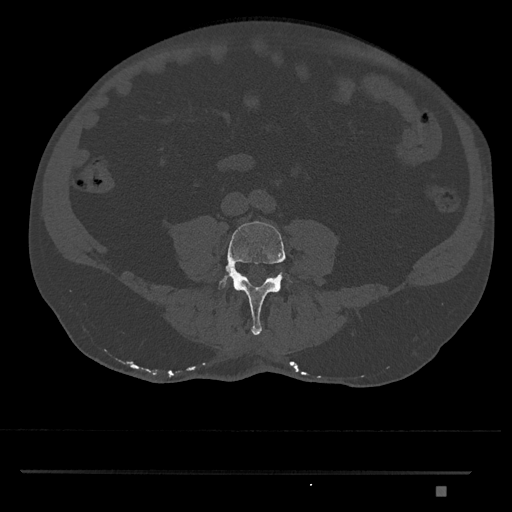
CT including the spine, one axial slice; slice 612 of 1134 in the series (ordered by position); bone window (W 1800 / L 400 HU); 0.5 mm slice thickness; 512 × 512 image matrix, field of view 429 × 429 mm. Patient: male, 65 years. From the clinical record (not read from this slice): primary cancer: prostate.
Outlined on this slice (semi-automatically segmented with operator editing):
- L4 vertebra: bounding box <218,221,292,335> (left, top, right, bottom; pixels)